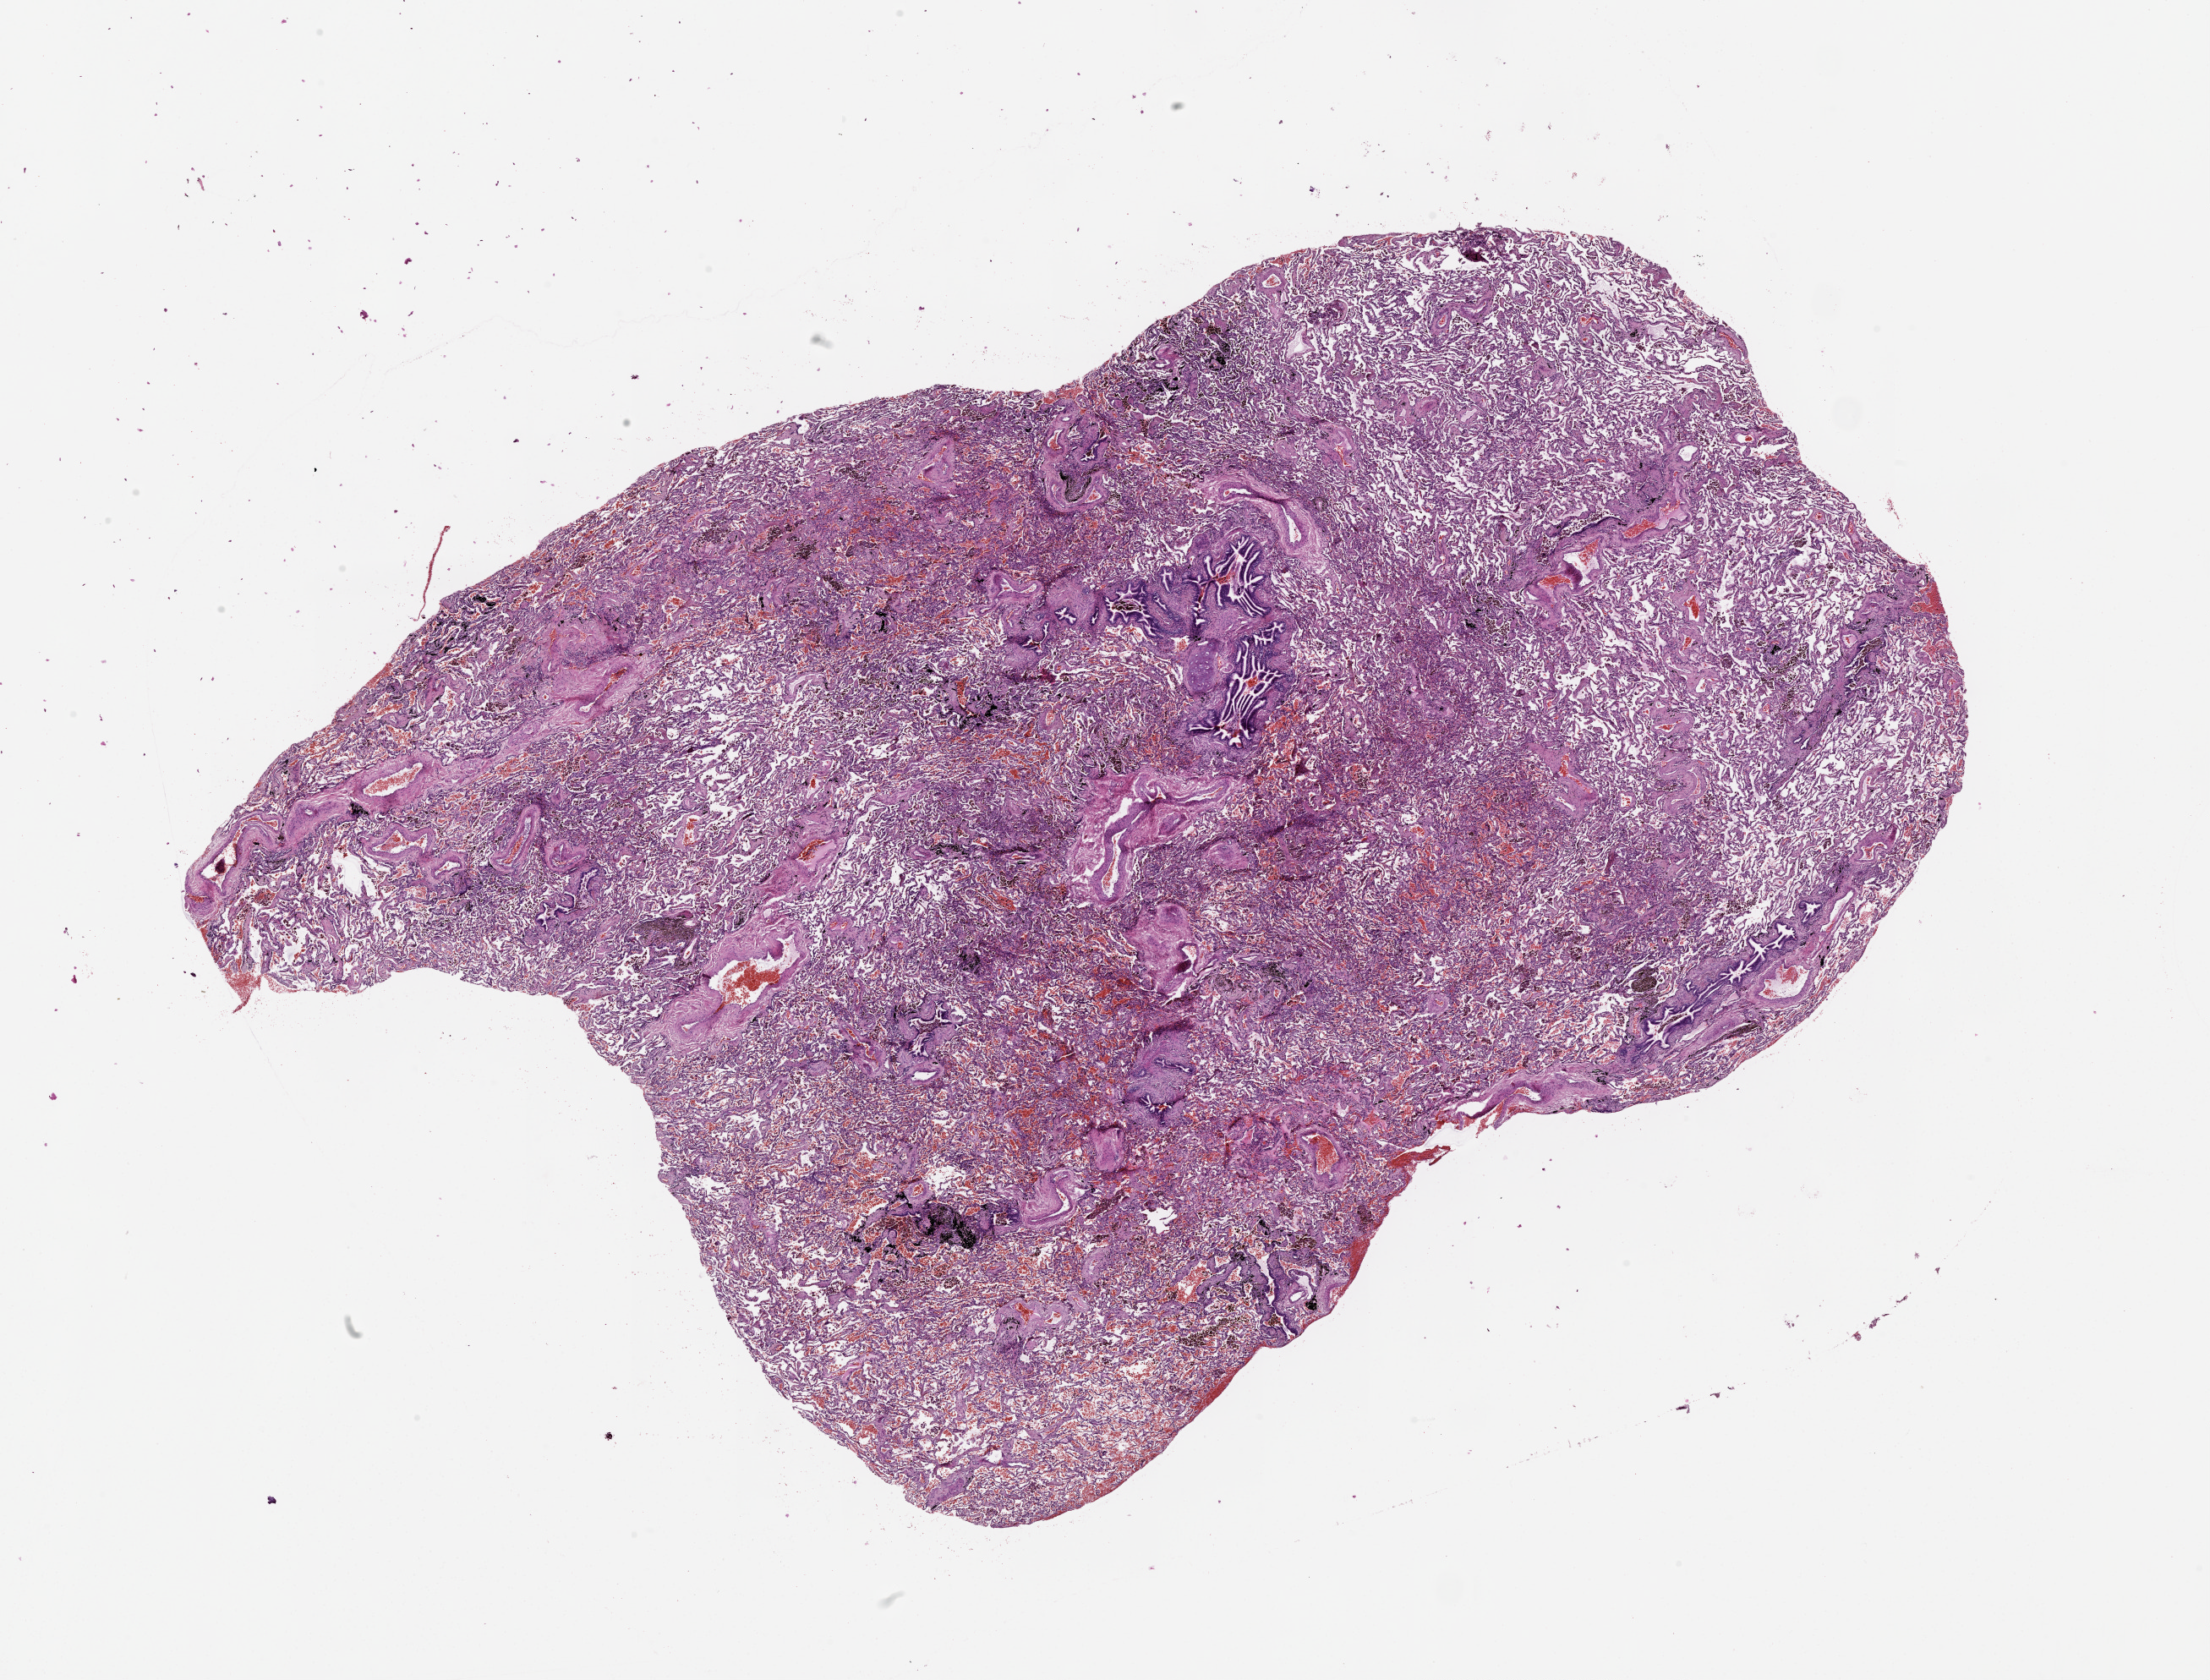
H&E whole-slide image — a low-resolution overview of the entire scanned area, about 21.0 x 16.0 mm, lung, normal (non-tumour) tissue. Patient: female, age 56 years.
* this section: normal (non-tumour) tissue from the same patient
* patient diagnosis (cohort enrolment): squamous cell carcinoma (lung)